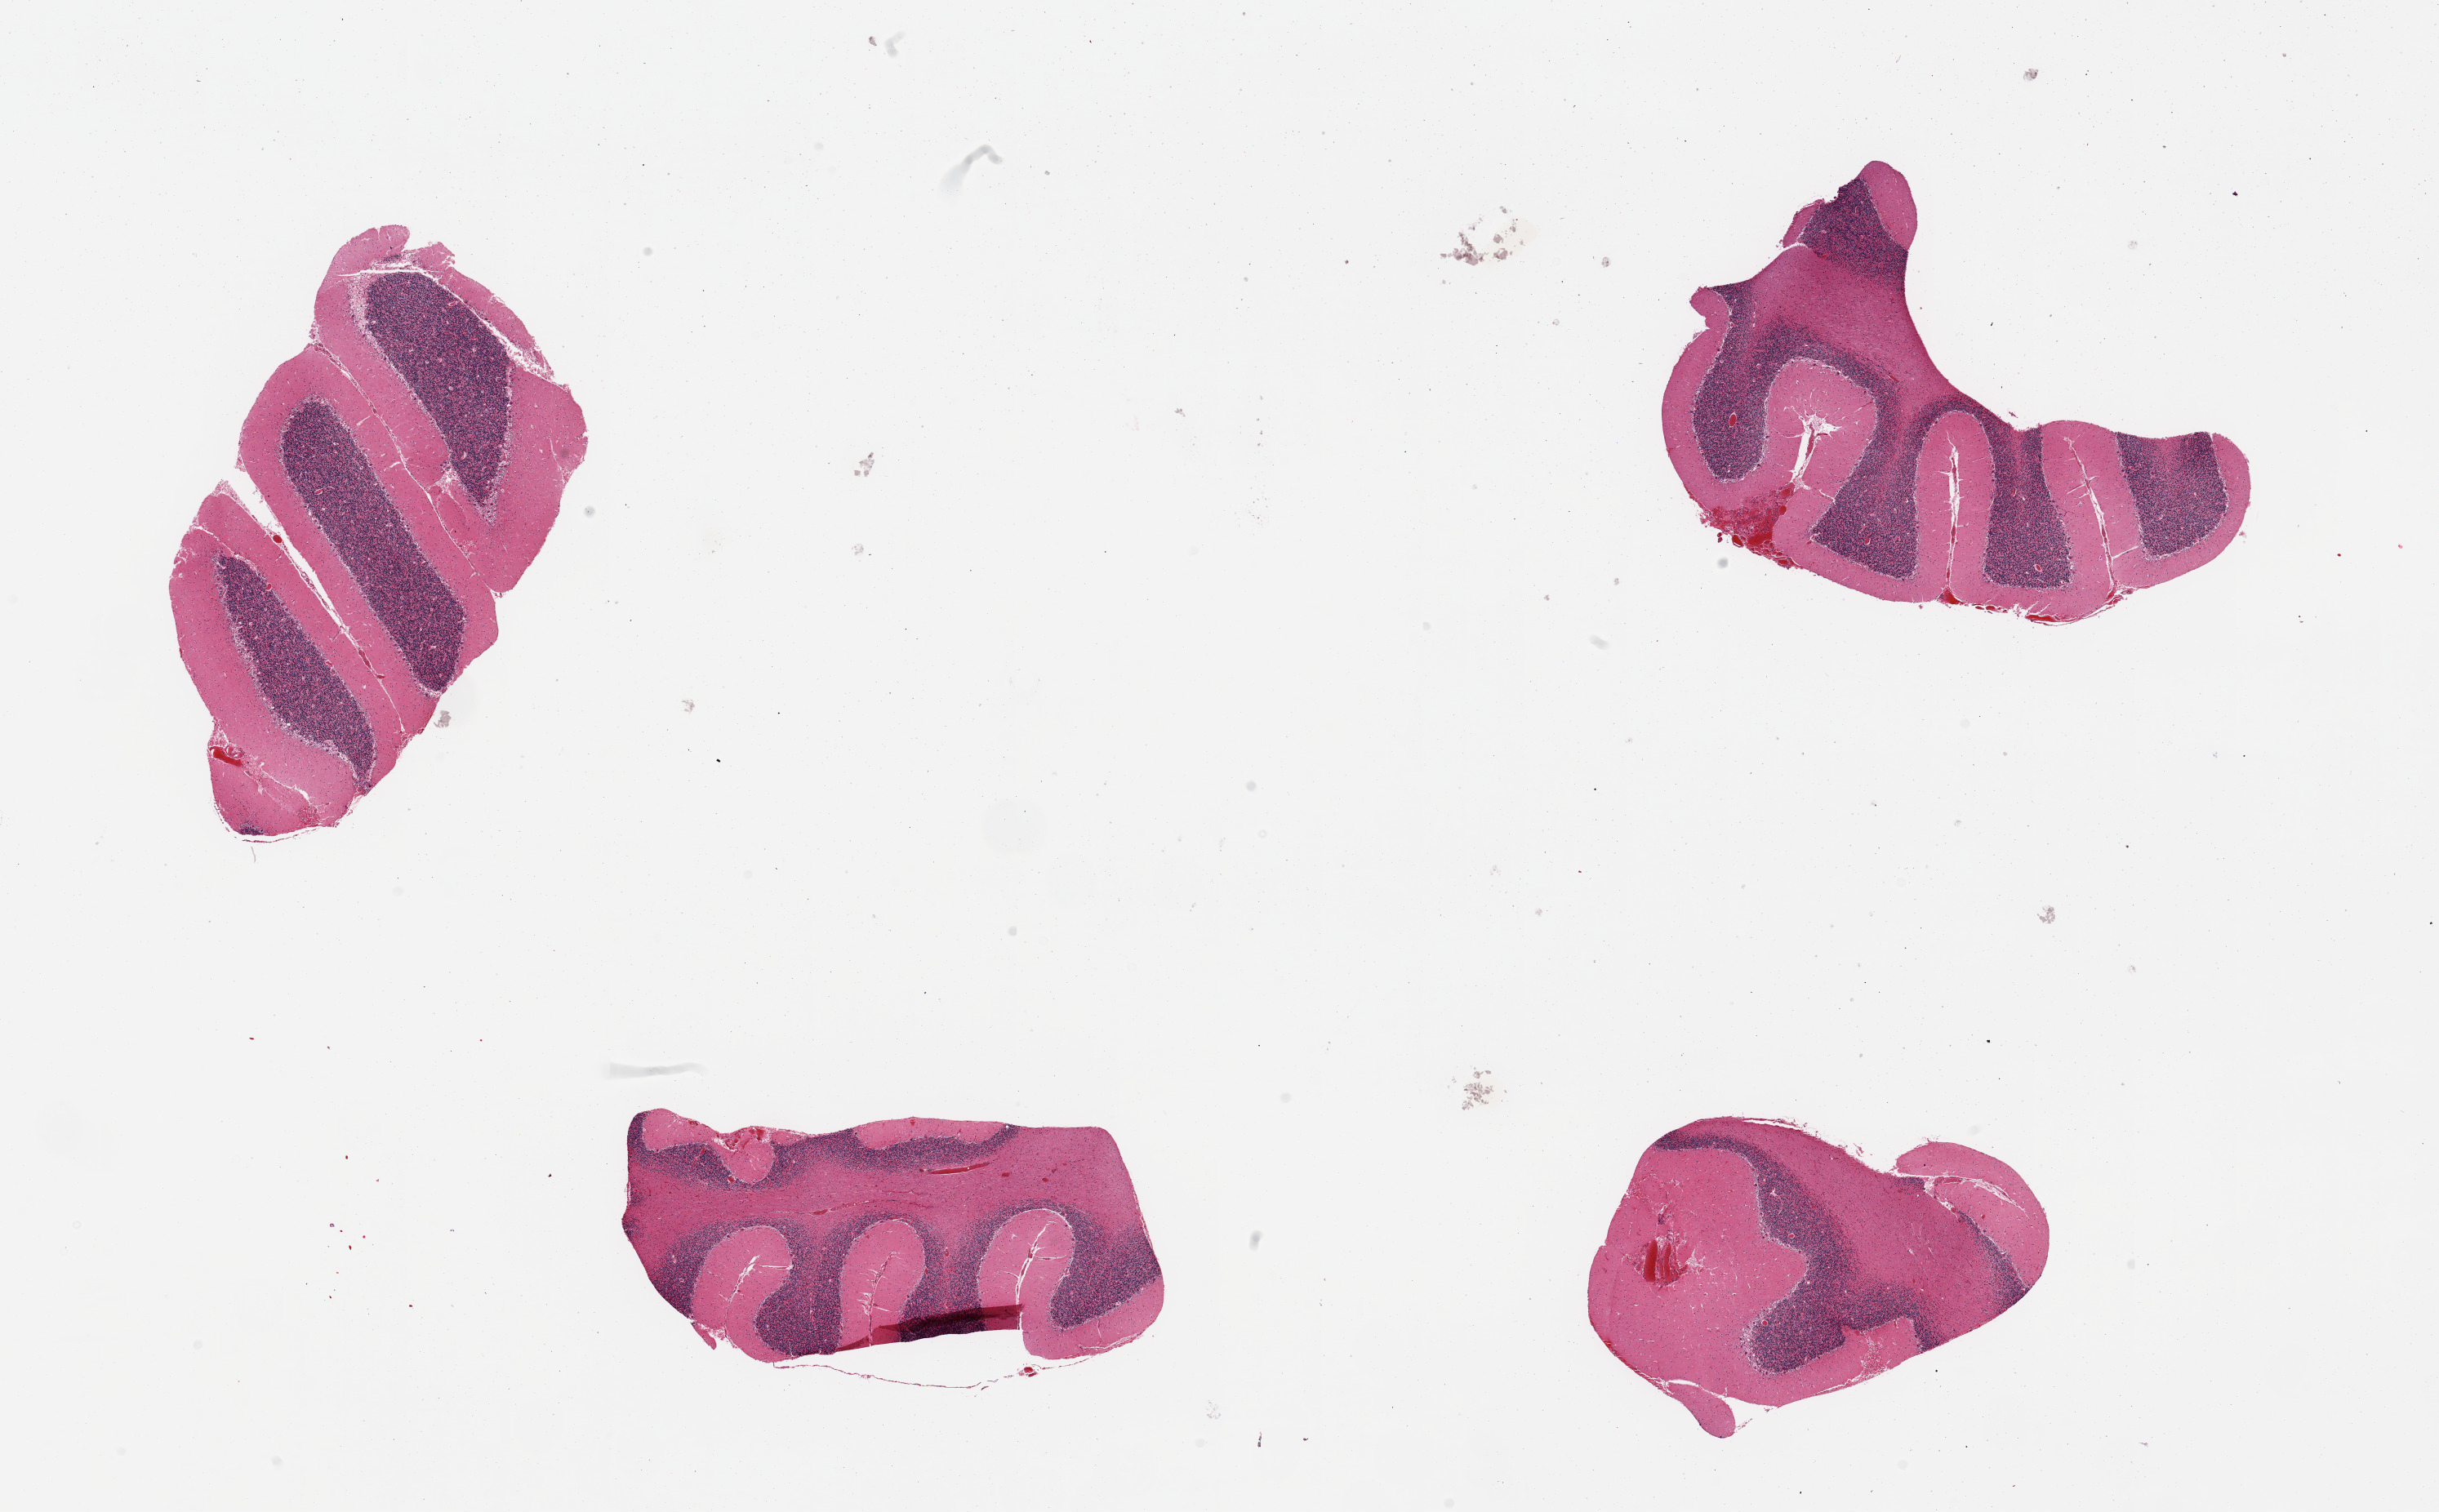
H&E whole-slide image, a low-resolution overview of the entire scanned area, about 23.6 x 14.6 mm (from a 20x scan), PAXgene-fixed paraffin-embedded (PFPE) section, target tissue: cerebellum, tissue donor sample. Donor sex: female.
- review note (as recorded): 4 pieces